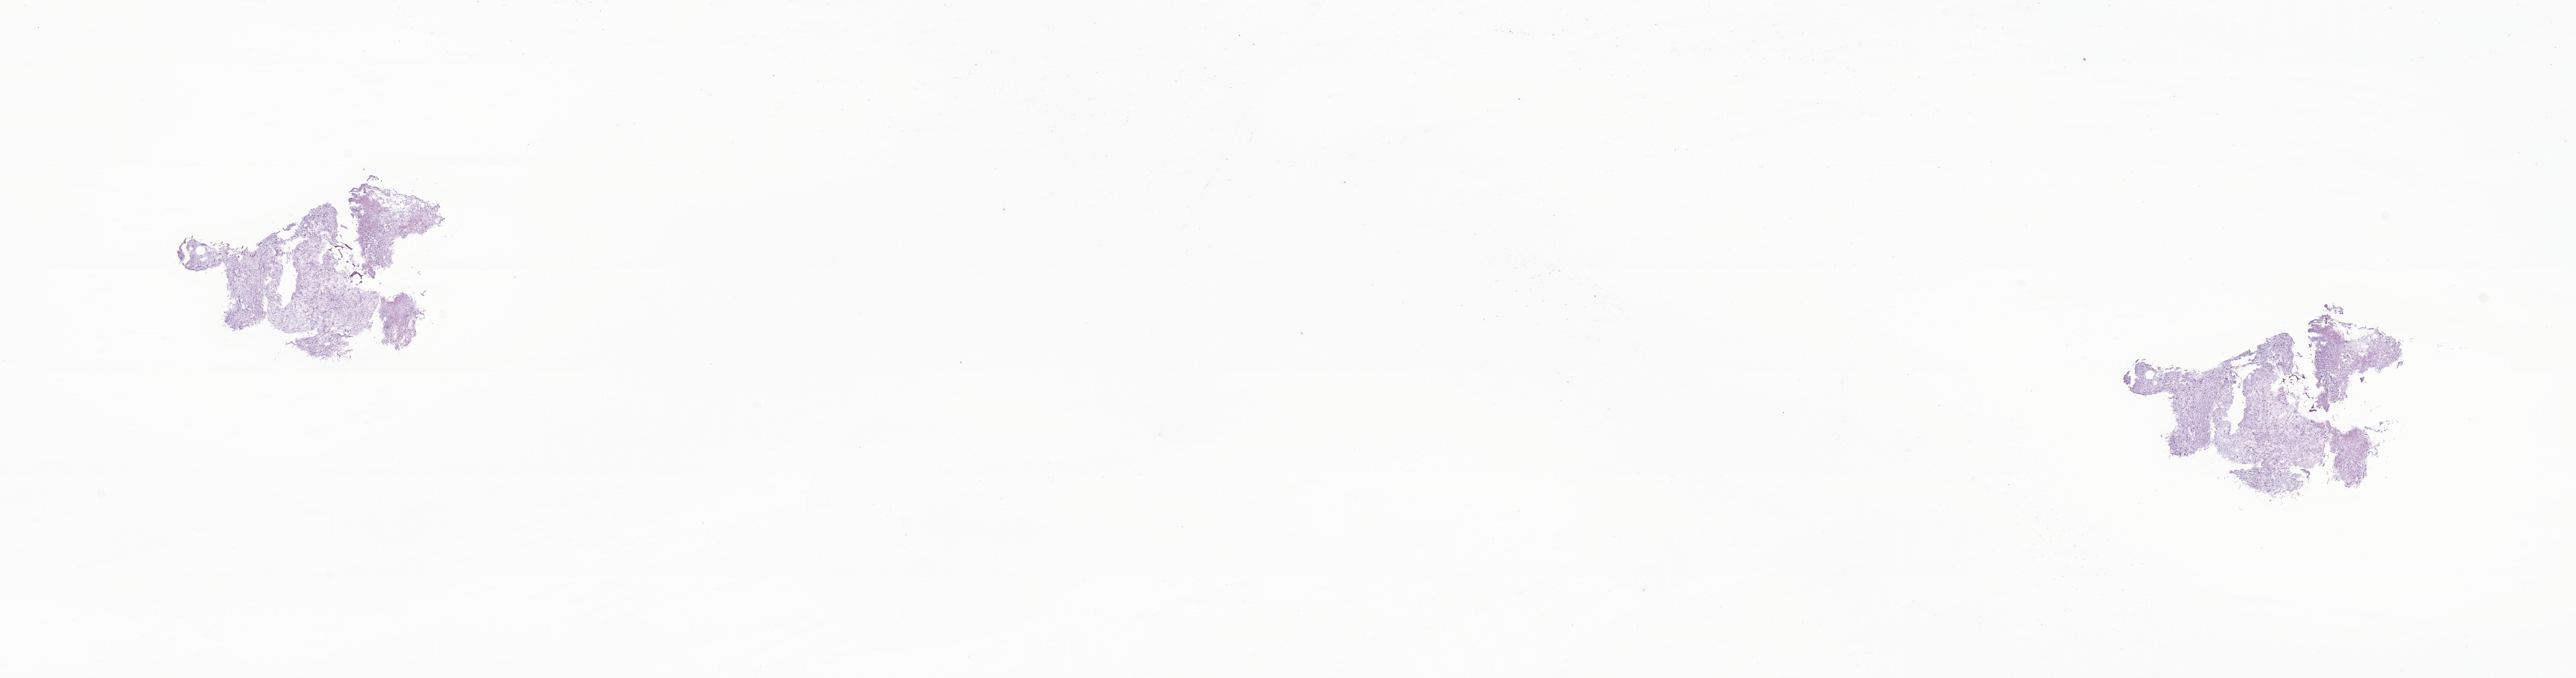
Haematoxylin and eosin whole-slide image of tumor tissue from the brain — whole scanned area (about 26.9 x 7.1 mm) shown as a low-resolution overview. Frozen section (OCT-embedded). Patient: female, age 126 months.
Recorded diagnosis: Pilocytic astrocytoma.